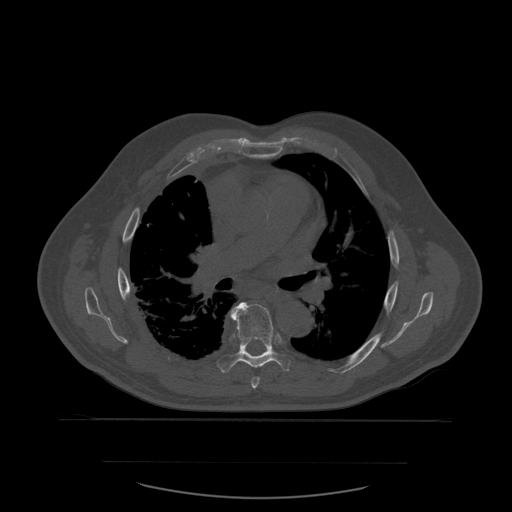
CT including the spine, one axial slice; position 386 of 590 along the scan axis; bone window (W 1800 / L 400 HU); 1.25 mm slice thickness; 512 × 512 image matrix, field of view 479 × 479 mm. Patient age 71 years. From the clinical record (not read from this slice): primary cancer: lung.
Structures marked on this image (semi-automatic segmentation, software-assisted and operator-edited):
- T6 vertebra: bounding box <252,377,260,389> (left, top, right, bottom; pixels)
- T7 vertebra: <217,302,295,373>